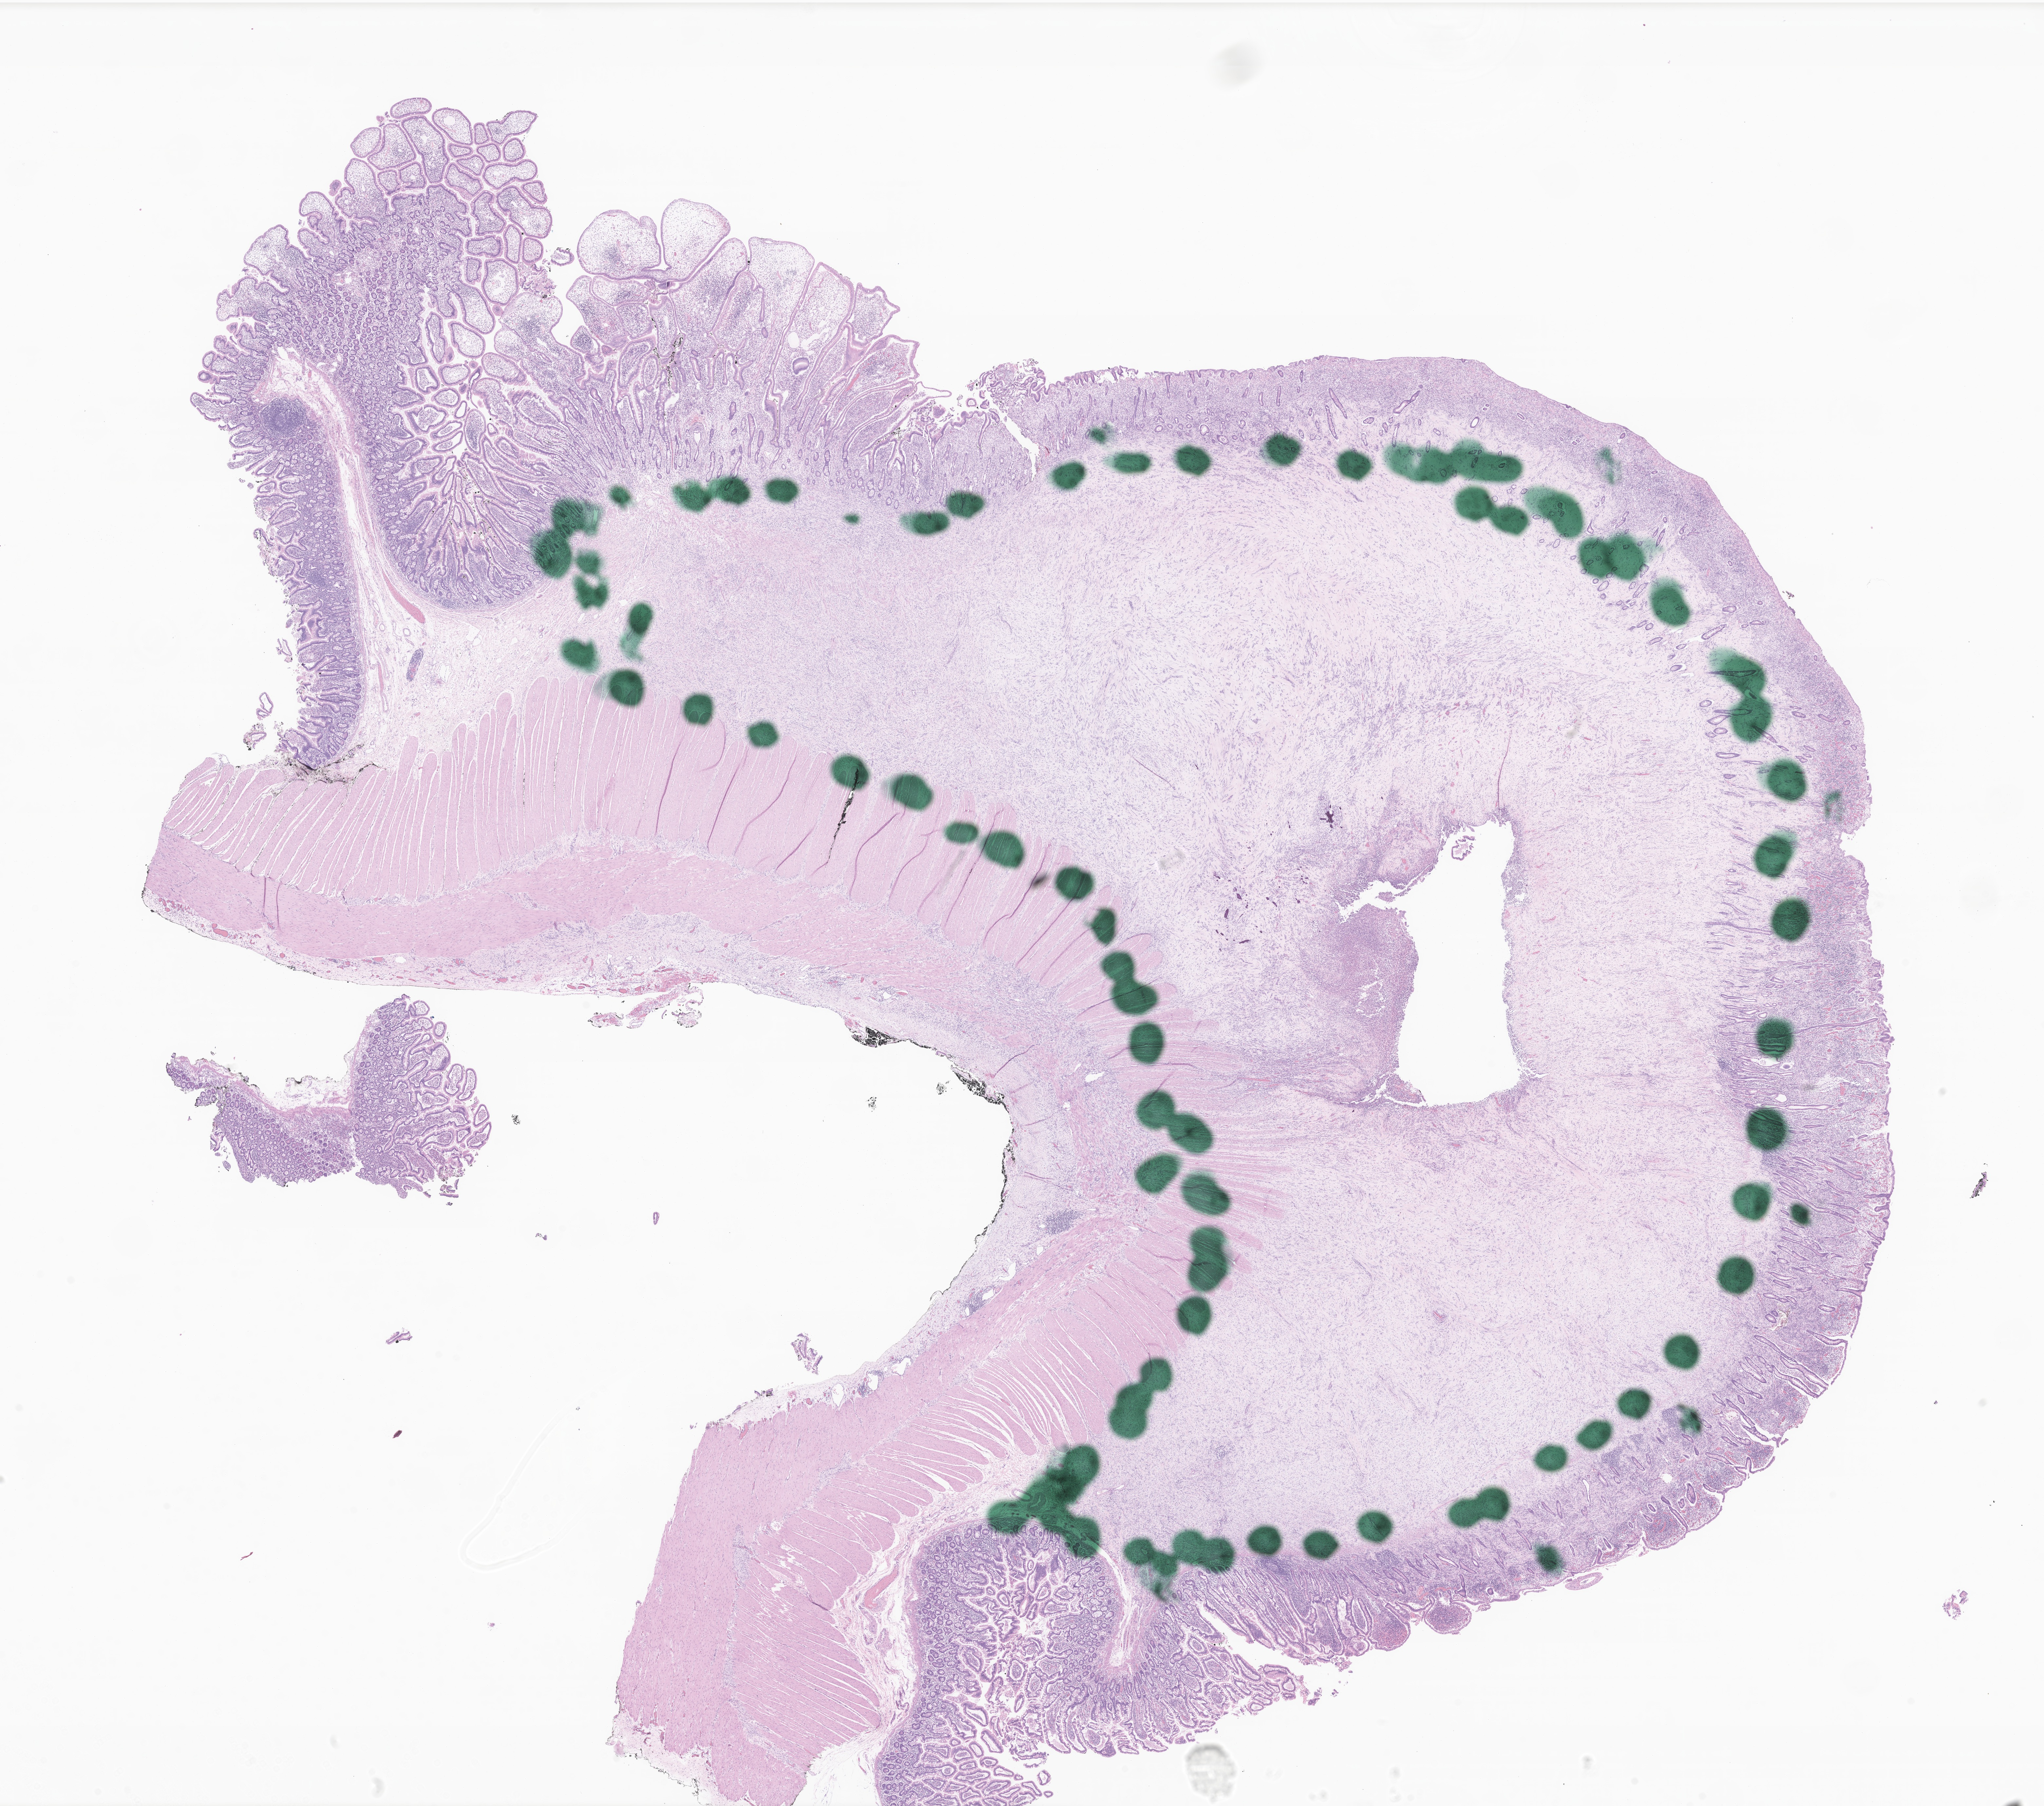
Digitized hematoxylin and eosin (H&E)-stained section of tumor tissue from the small intestine, shown as a low-resolution overview of the whole scanned area (about 26.3 x 23.2 mm). FFPE section. Patient male; age 162 months.
Diagnosis: Myofibroblastic tumor, NOS.